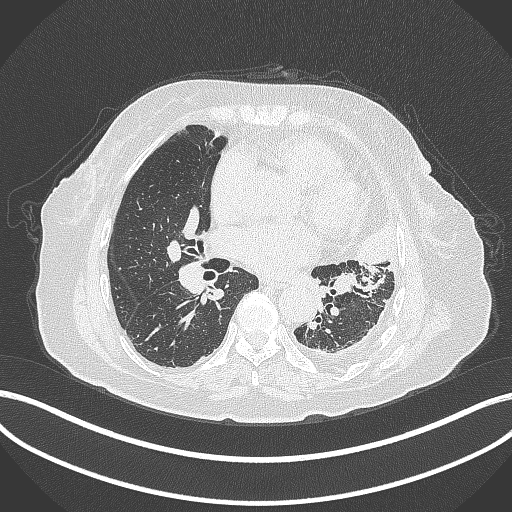
Chest CT, one axial slice; slice 175 of 399 in the series (ordered by position); reconstruction kernel B70f; 120 kVp; lung window (W 1500 / L -600 HU); 512 × 512 image matrix. Patient: female, 75 years. From the clinical record (not read from this slice): clinical TNM (as recorded): T3 N3 M1.
Outlined on this slice (bounding box drawn by a radiologist):
- lung tumour (recorded histology: adenocarcinoma): bounding box [x1, y1, x2, y2] px = [351, 221, 408, 276]